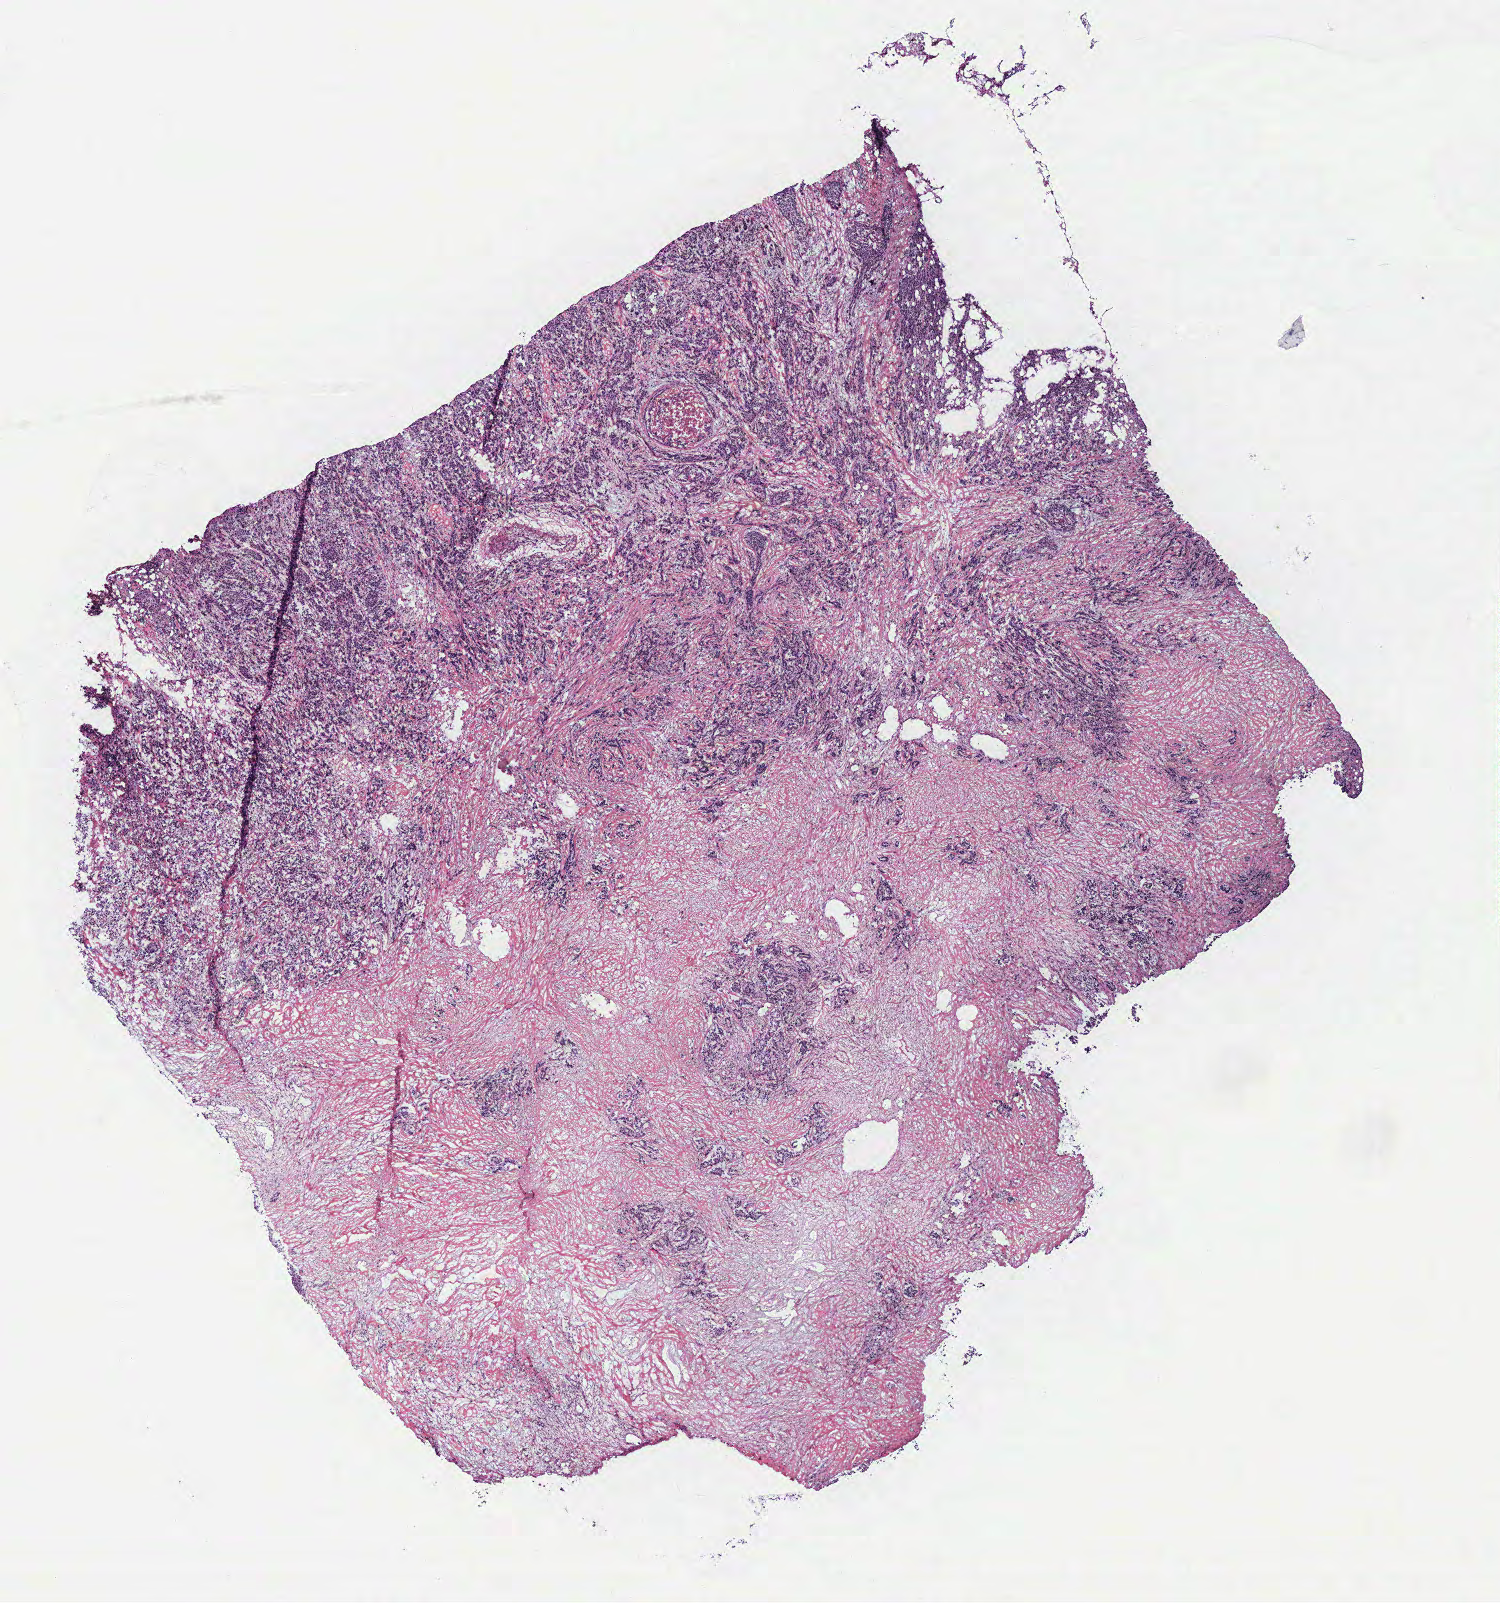
Hematoxylin and eosin (H&E) stained whole-slide image — shown as a low-resolution overview of the whole scanned area (about 12.0 x 12.8 mm); breast, tissue type not recorded. Female, 45 y/o.
Patient diagnosis: Infiltrating duct and lobular carcinoma.